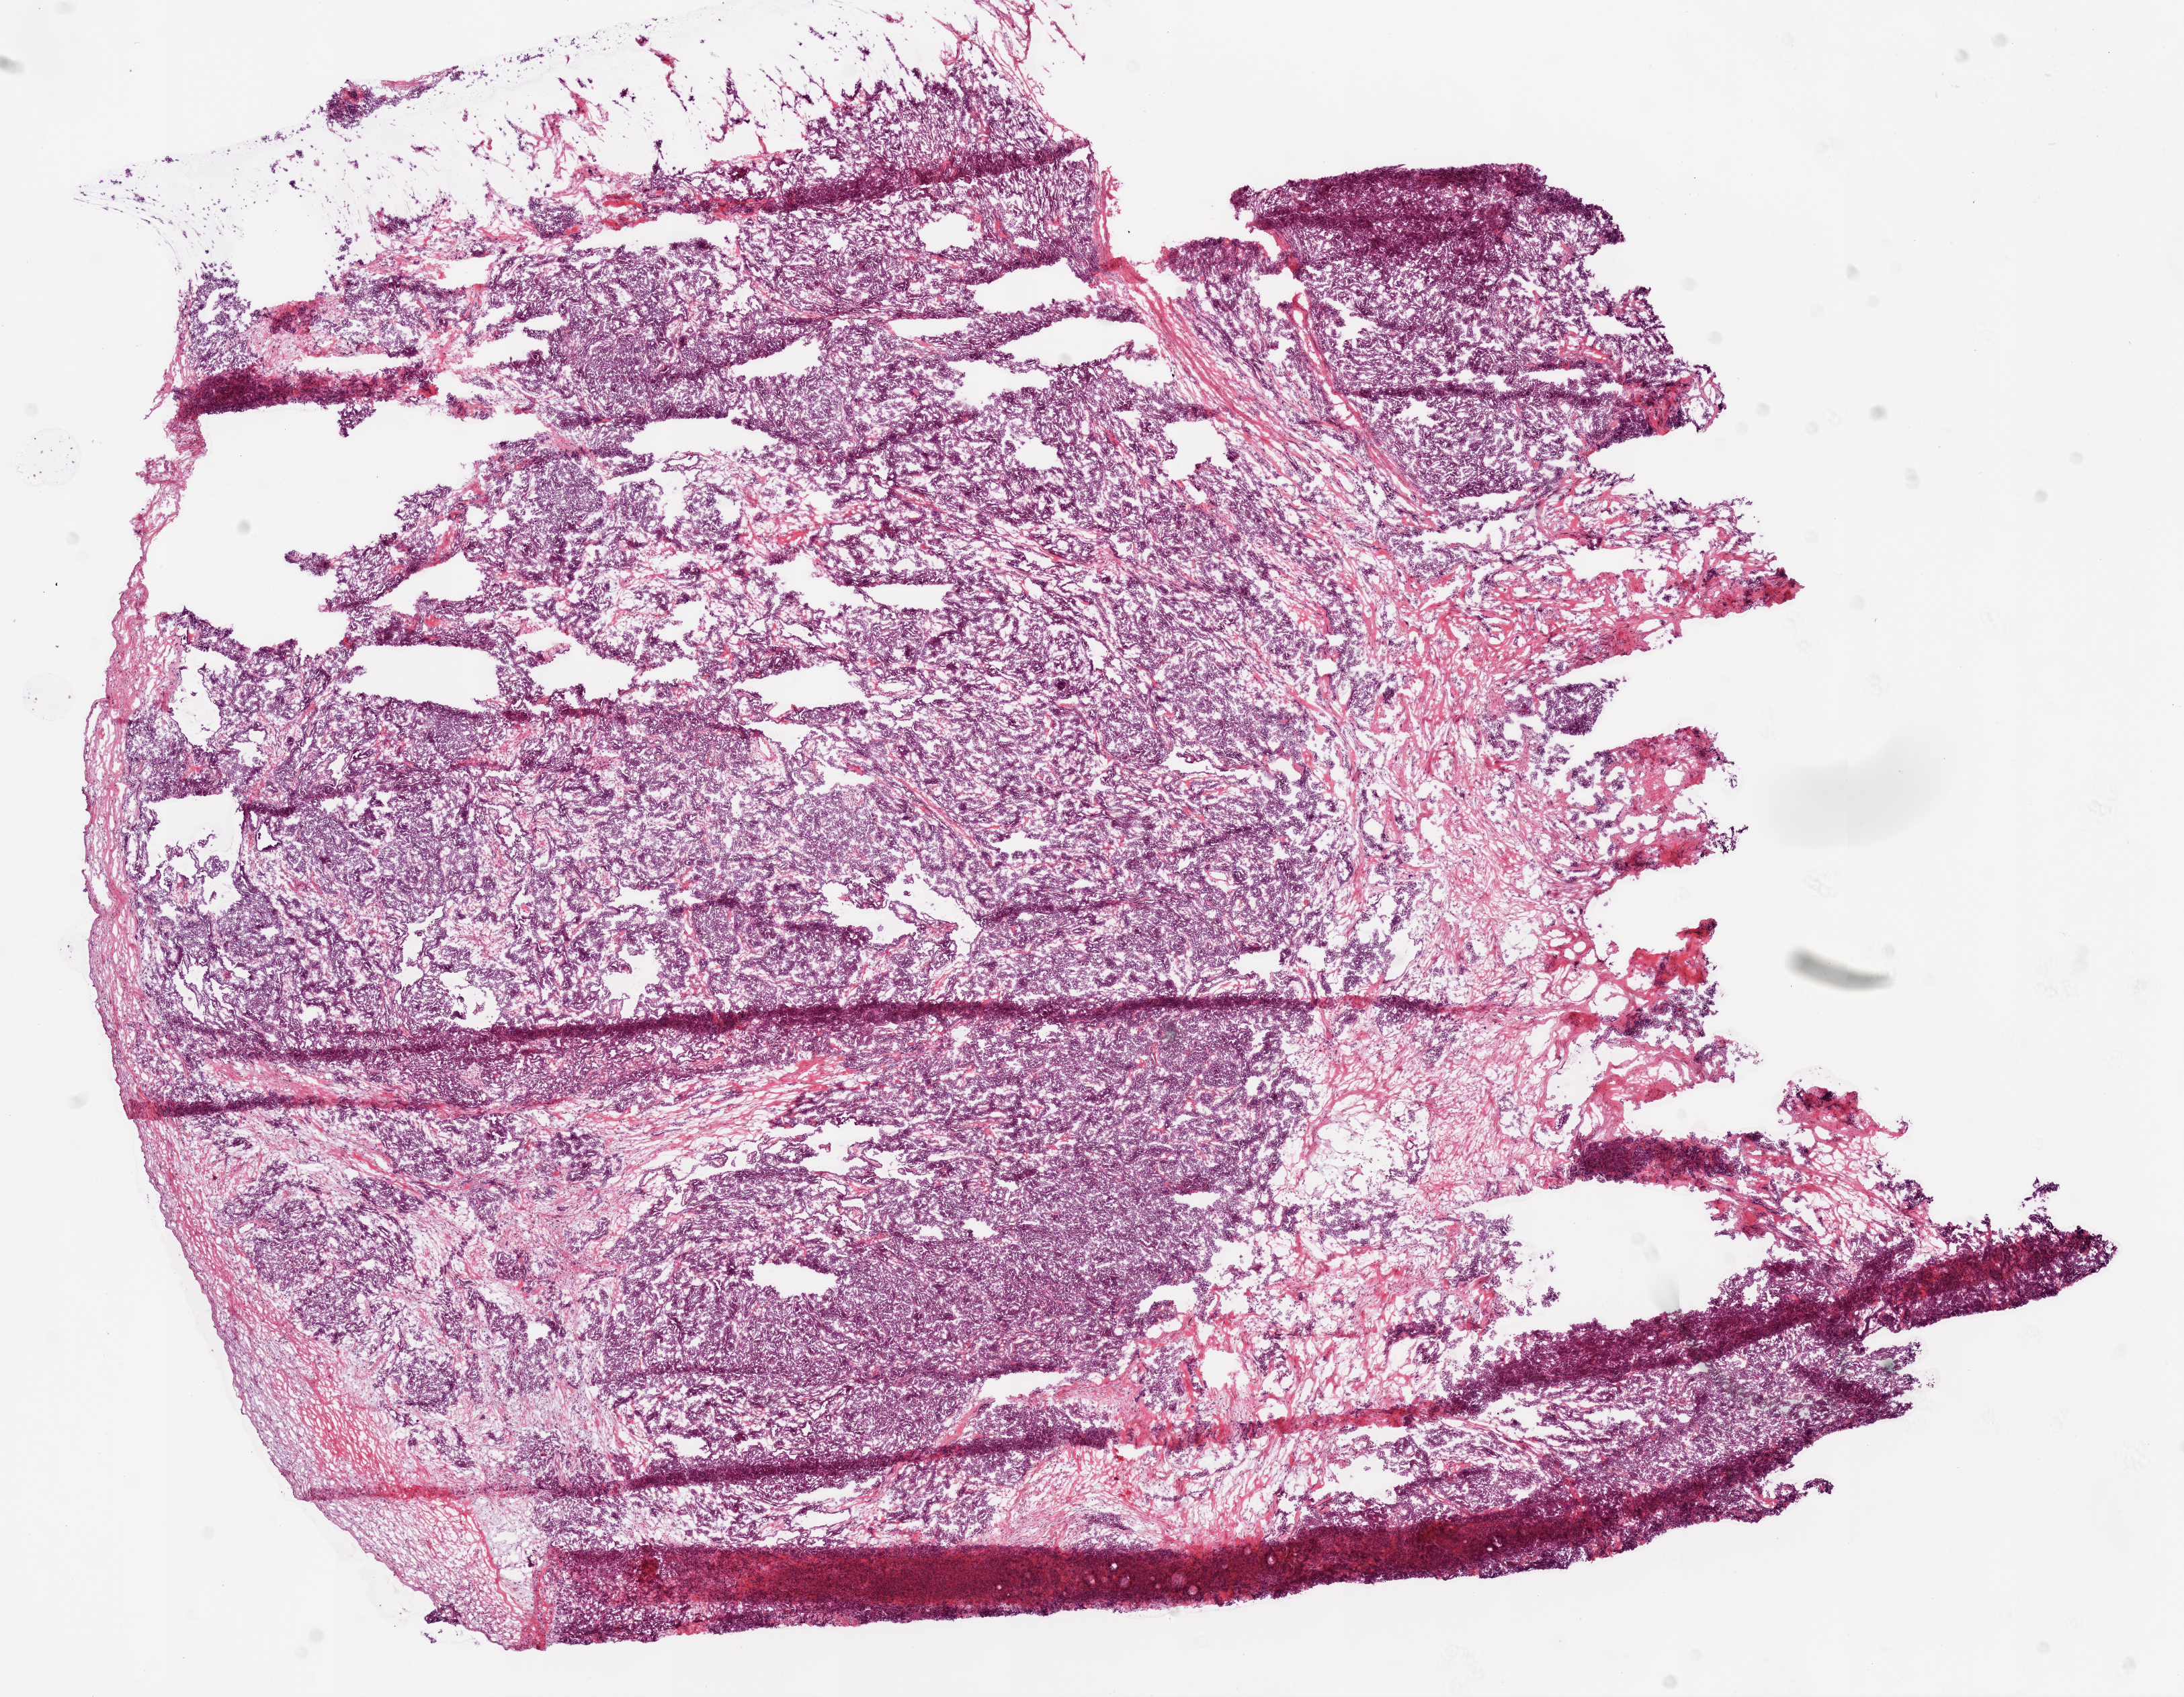
Whole-slide histology image, H&E-stained — shown as a low-resolution overview of the whole scanned area (about 13.0 x 10.1 mm, slide scanned at 20x). Frozen section. Ovary, primary tumour sample. Female patient; age at initial diagnosis 53 years. Histologic grade: G3 (poorly differentiated). Composition of this section per pathologist review: tumour cells 85%, tumour nuclei 95%, normal cells 0%, stromal cells 15%, necrosis 0%.
- pathologic diagnosis: Serous cystadenocarcinoma, NOS
- laterality: bilateral
- FIGO stage: IIIB